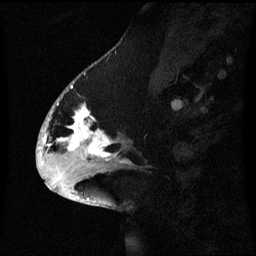
Breast MRI (dynamic contrast-enhanced), one sagittal slice; slice 26 of 60 in the series (ordered by position); dynamic contrast-enhanced series, image 2 of 3 at this slice position (ordered by acquisition); 1.5 T; TE 4.2 ms, TR 8.4 ms; 256 × 256 image matrix, field of view 220 × 220 mm. Patient: female, 53 years. Case-level facts recorded for this patient, not image findings: setting: breast cancer imaged before/during neoadjuvant chemotherapy; receptor status: HR-positive, HER2-negative.
Annotated regions visible in this slice (semi-automatic segmentation, software-assisted and operator-edited):
- analysis volume of interest (the breast-tissue region the enhancement analysis was run in; not a lesion): bounding box [x1, y1, x2, y2] px = [52, 90, 131, 171]
- tumour enhancement mask (voxels above the 70 % enhancement threshold inside the analysis volume of interest): [52, 104, 123, 163]